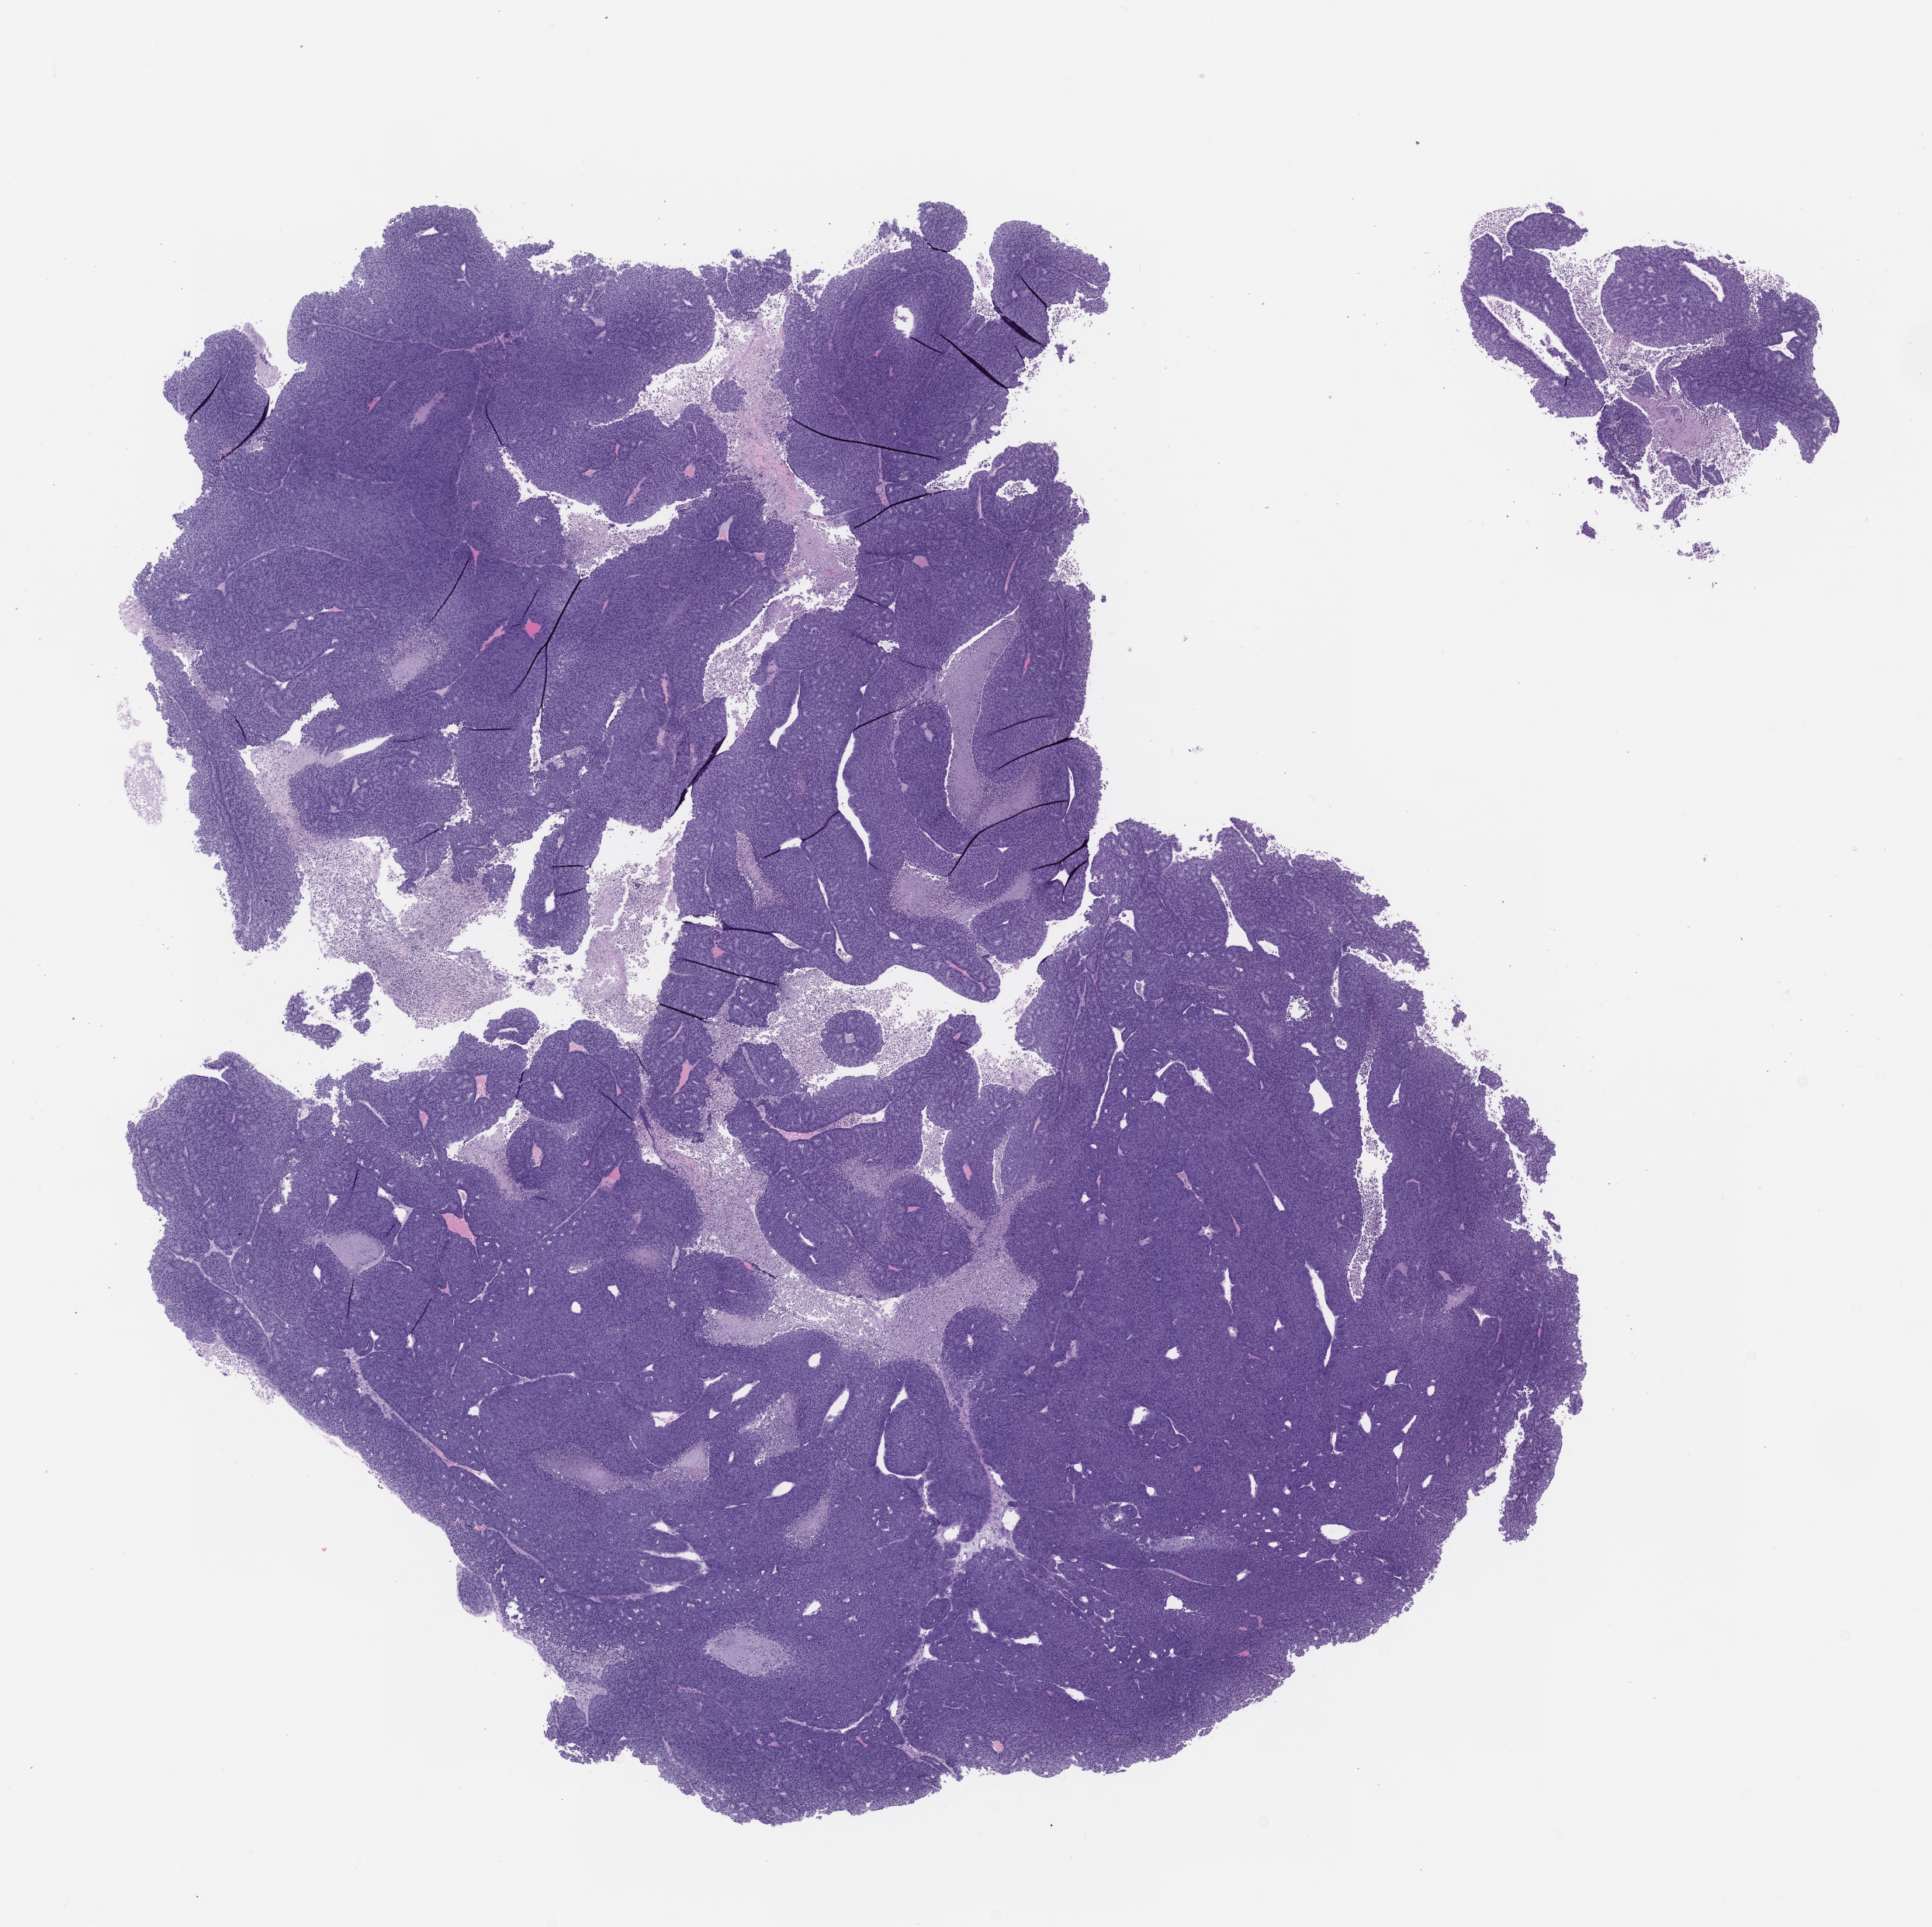
Haematoxylin and eosin whole-slide image of a patient-derived xenograft (PDX) tumor grown in a mouse, passage 0 — low-resolution overview of the scanned area, about 10.0 x 10.0 mm; FFPE section; tumor site category: head and neck.
Originating patient diagnosis: Acinar Cell Carcinoma.